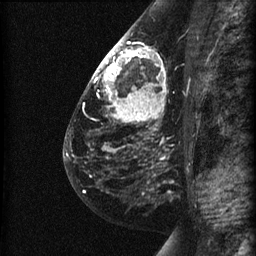
Breast MRI (dynamic contrast-enhanced), one sagittal slice; dynamic contrast-enhanced series, image 2 of 3 at this slice position (ordered by acquisition); 1.5 T; TE 4.2 ms, TR 22.7 ms; 1.5 mm slice thickness; 256 × 256 image matrix. Female patient, age 48 years. From the clinical record (not read from this slice): setting: breast cancer imaged before/during neoadjuvant chemotherapy; receptor status: triple-negative.
Annotated regions visible in this slice (semi-automatically segmented with operator editing):
- analysis volume of interest (the breast-tissue region the enhancement analysis was run in; not a lesion): bounding box (x1, y1, x2, y2) in pixels: (89, 27, 191, 180)
- tumour enhancement mask (voxels above the 90 % enhancement threshold inside the analysis volume of interest): (93, 38, 165, 110)